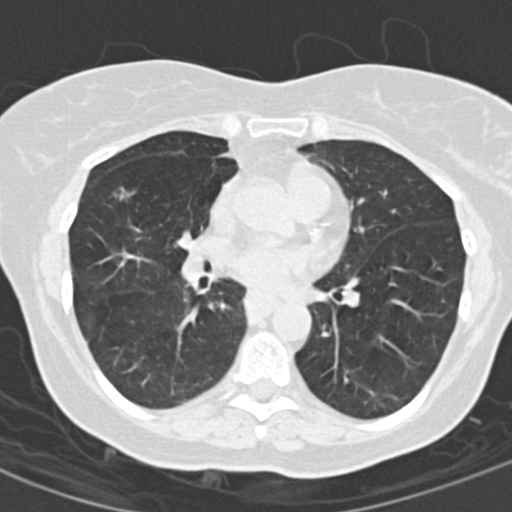
Low-dose screening chest CT, one axial slice; position 74 of 154 along the scan axis; reconstruction kernel B30f; lung window (W 1500 / L -600 HU); 2 mm slice thickness; 512 × 512 image matrix.
Outlined on this slice (expert manual segmentation):
- lesion 2 (nodule, middle lobe of right lung): box from (x=115, y=188) to (x=129, y=200) px